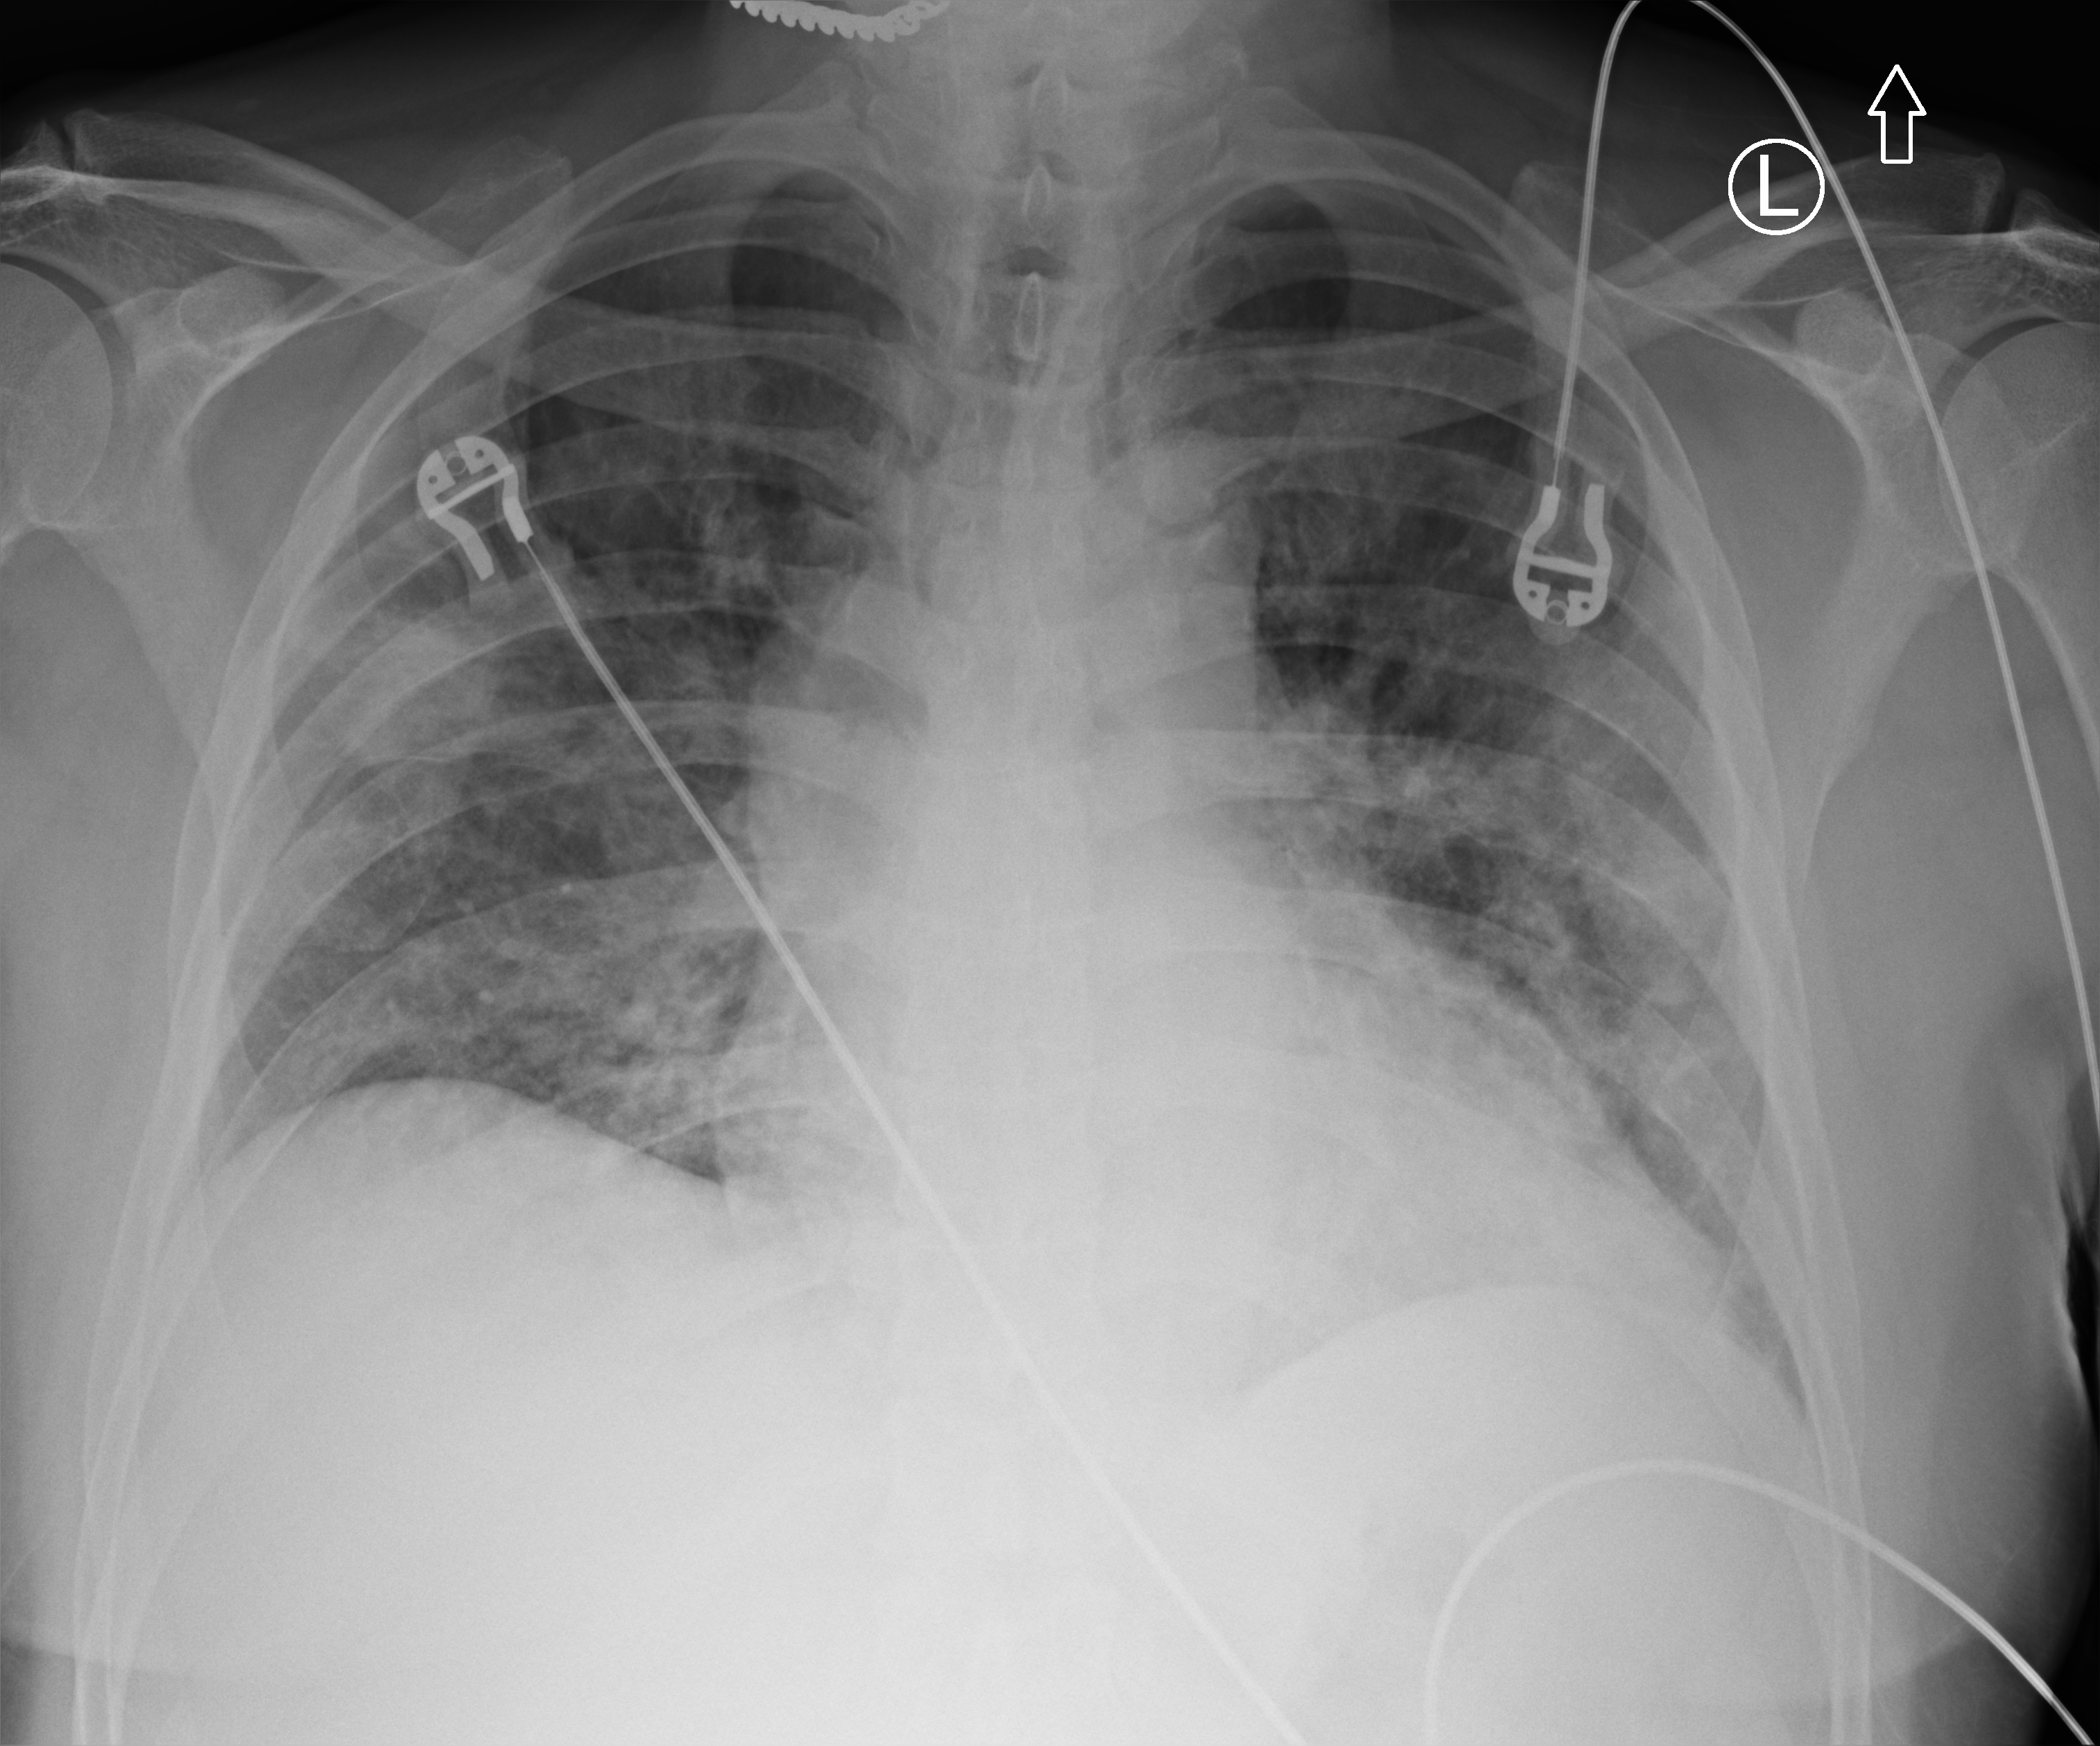
Bedside chest radiograph (computed radiography), anteroposterior (AP) projection. Male patient hospitalised with COVID-19, age 60–74 years.
From the hospital-stay record, not from the radiograph (when in the stay this image was taken is not recorded): admitted to intensive care during this hospital stay: no; hypertension (admission record): no; mechanically ventilated during this hospital stay: no.